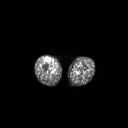
FDG PET of an extremity soft-tissue mass (from a PET/CT study), one axial slice. Slice 239 of 311 in the series (ordered by position). 3.27 mm slice thickness. 128 × 128 image matrix, field of view 700 × 700 mm. Male patient, age 56 years. Case-level facts recorded for this patient, not image findings: histological type: pleiomorphic leiomyosarcoma; grade: intermediate; site of the primary tumour: right thigh.
Annotated regions visible in this slice (expert contour drawn on MRI and transferred to this co-registered scan by the dataset authors):
- gross tumour volume including surrounding oedema: box from (x=45, y=58) to (x=51, y=62) px